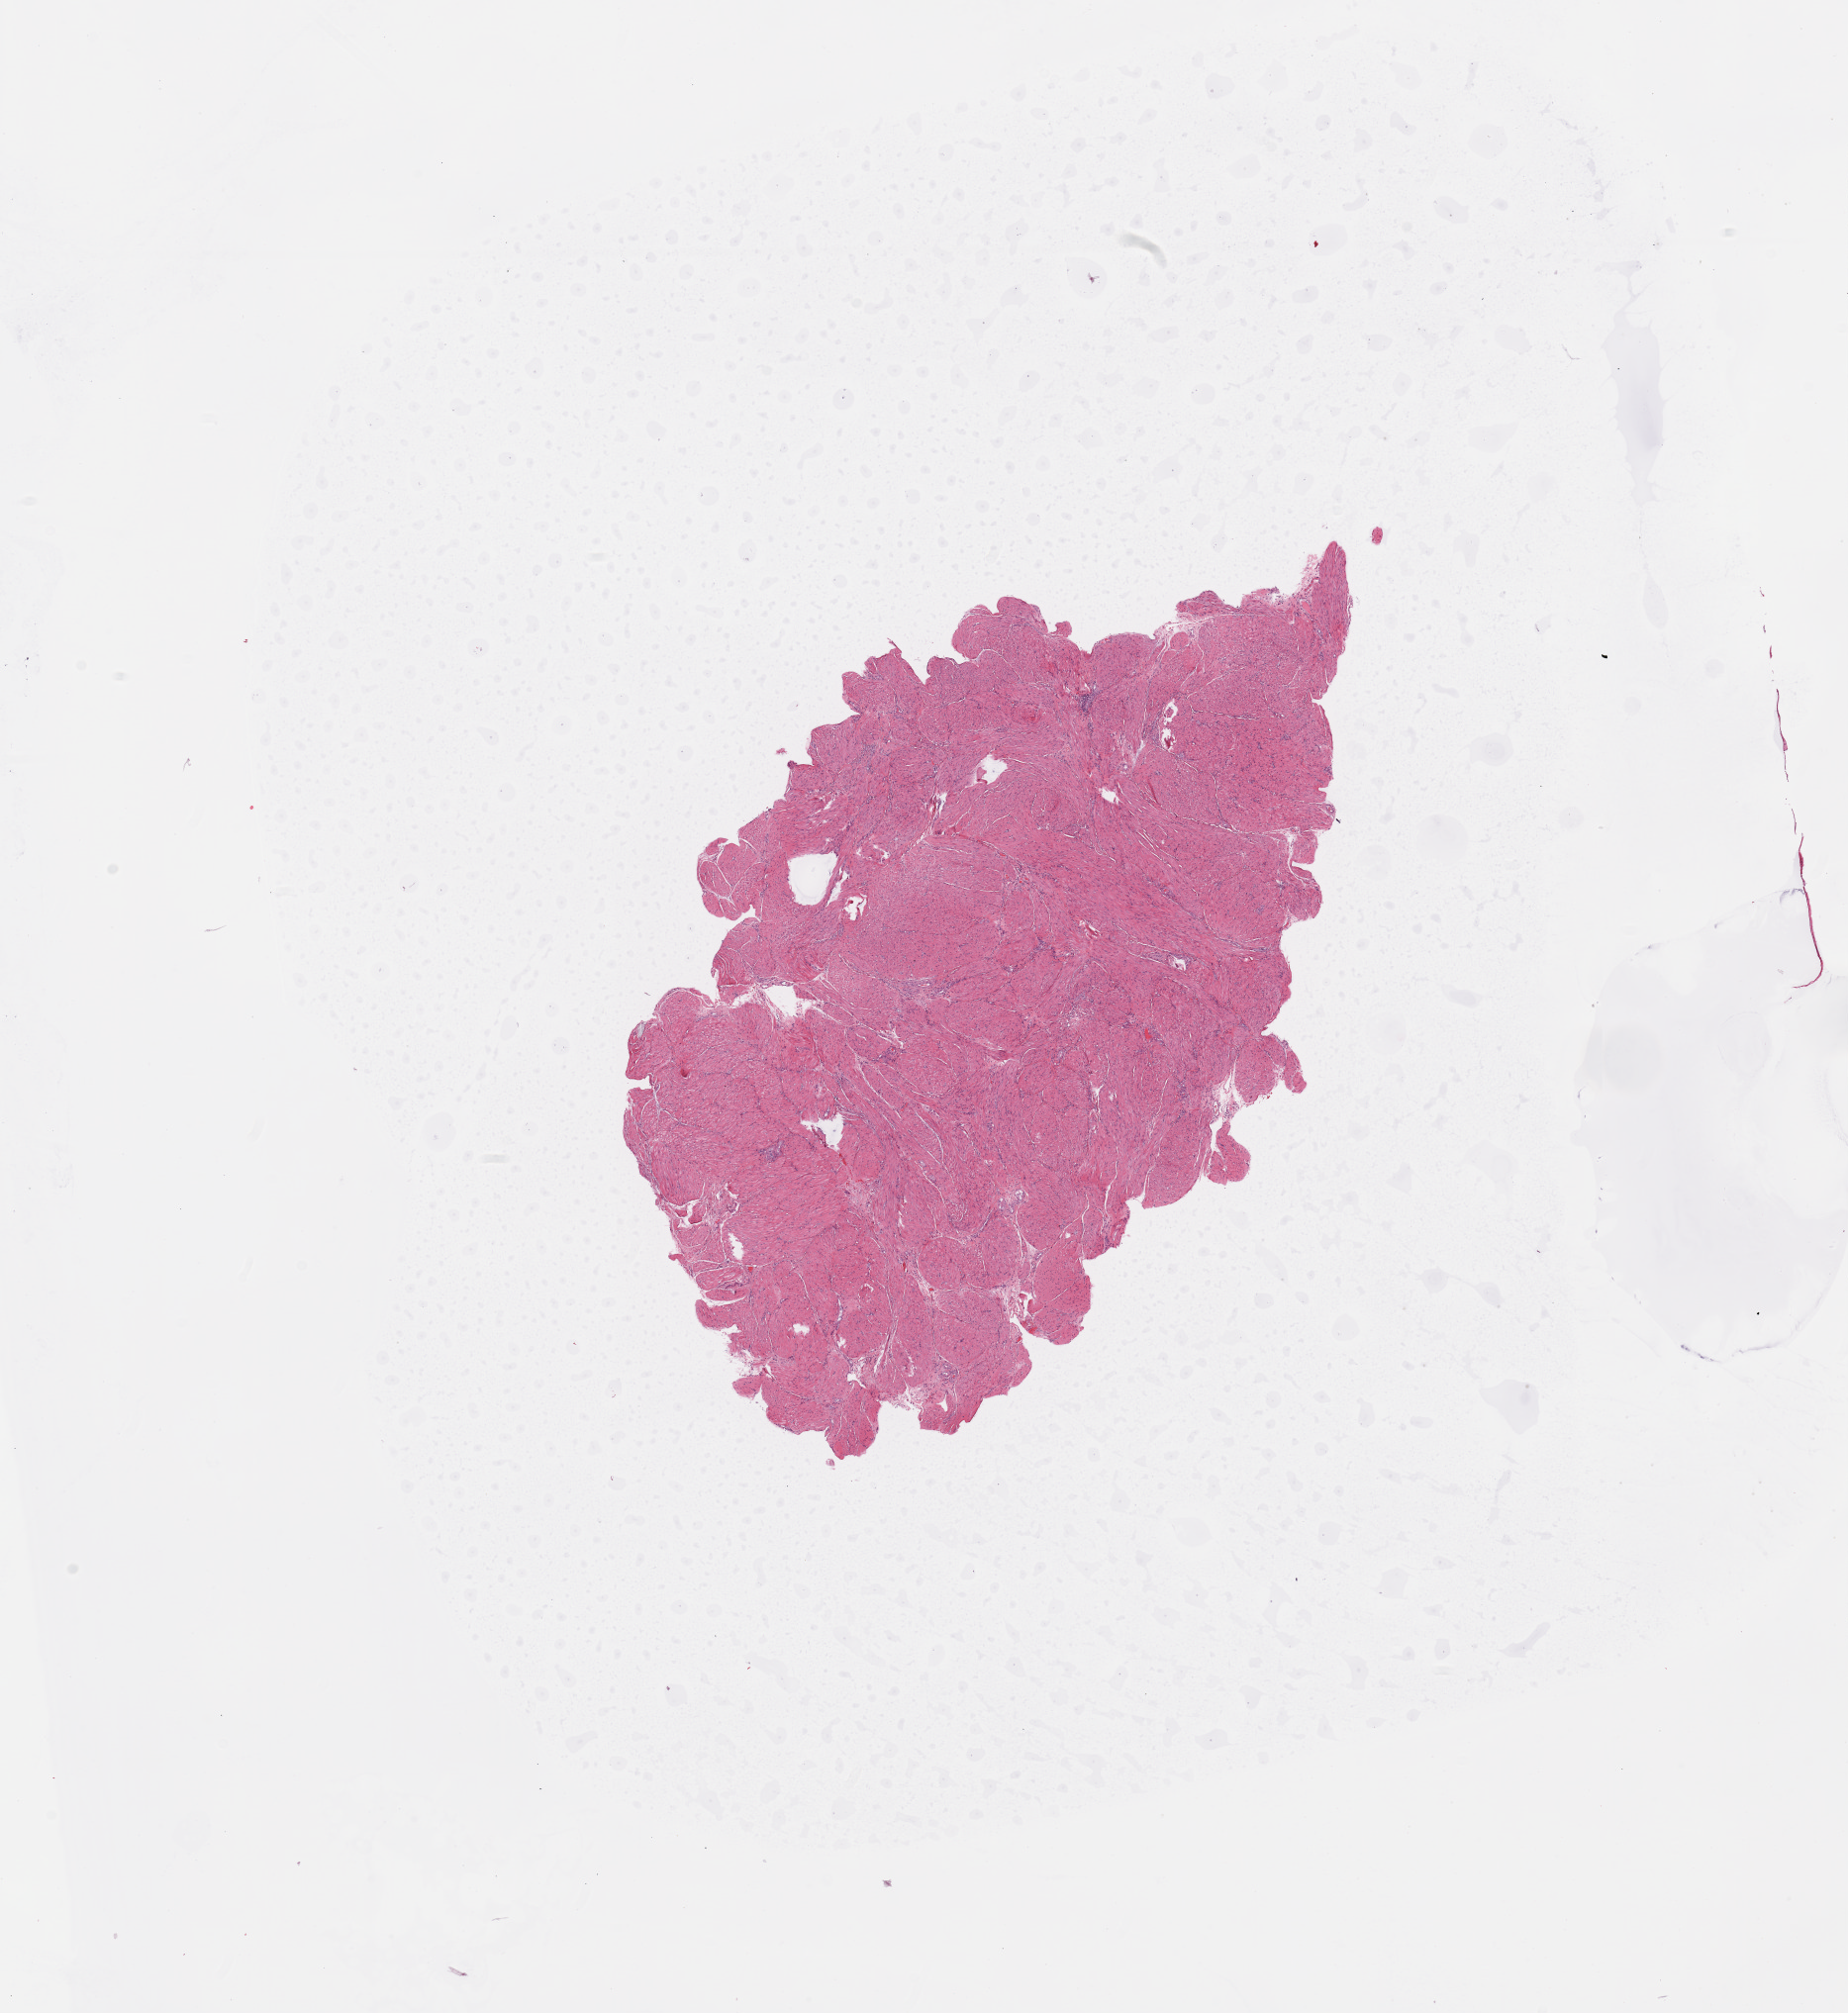
Whole-slide histology image, H&E-stained, whole scanned area (about 14.8 x 16.1 mm, acquisition: 20x scan) shown as a low-resolution overview. Normal (non-tumour) tissue sample, uterus. Female, 46 y/o.
This section: normal (non-tumour) tissue from the same patient. Patient diagnosis: Endometrioid adenocarcinoma, NOS.